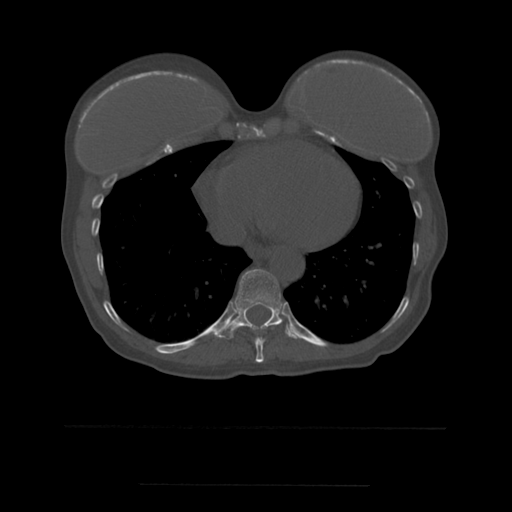
CT including the spine, one axial slice; position 309 of 544 along the scan axis; bone window (W 1800 / L 400 HU); 1.25 mm slice thickness; 512 × 512 image matrix, field of view 350 × 350 mm. Patient age 58 years. From the clinical record (not read from this slice): primary cancer: lung.
Structures marked on this image (semi-automatically segmented with operator editing):
- T10 vertebra: bounding box [x1, y1, x2, y2] px = [217, 269, 298, 339]
- T9 vertebra: [255, 325, 277, 363]